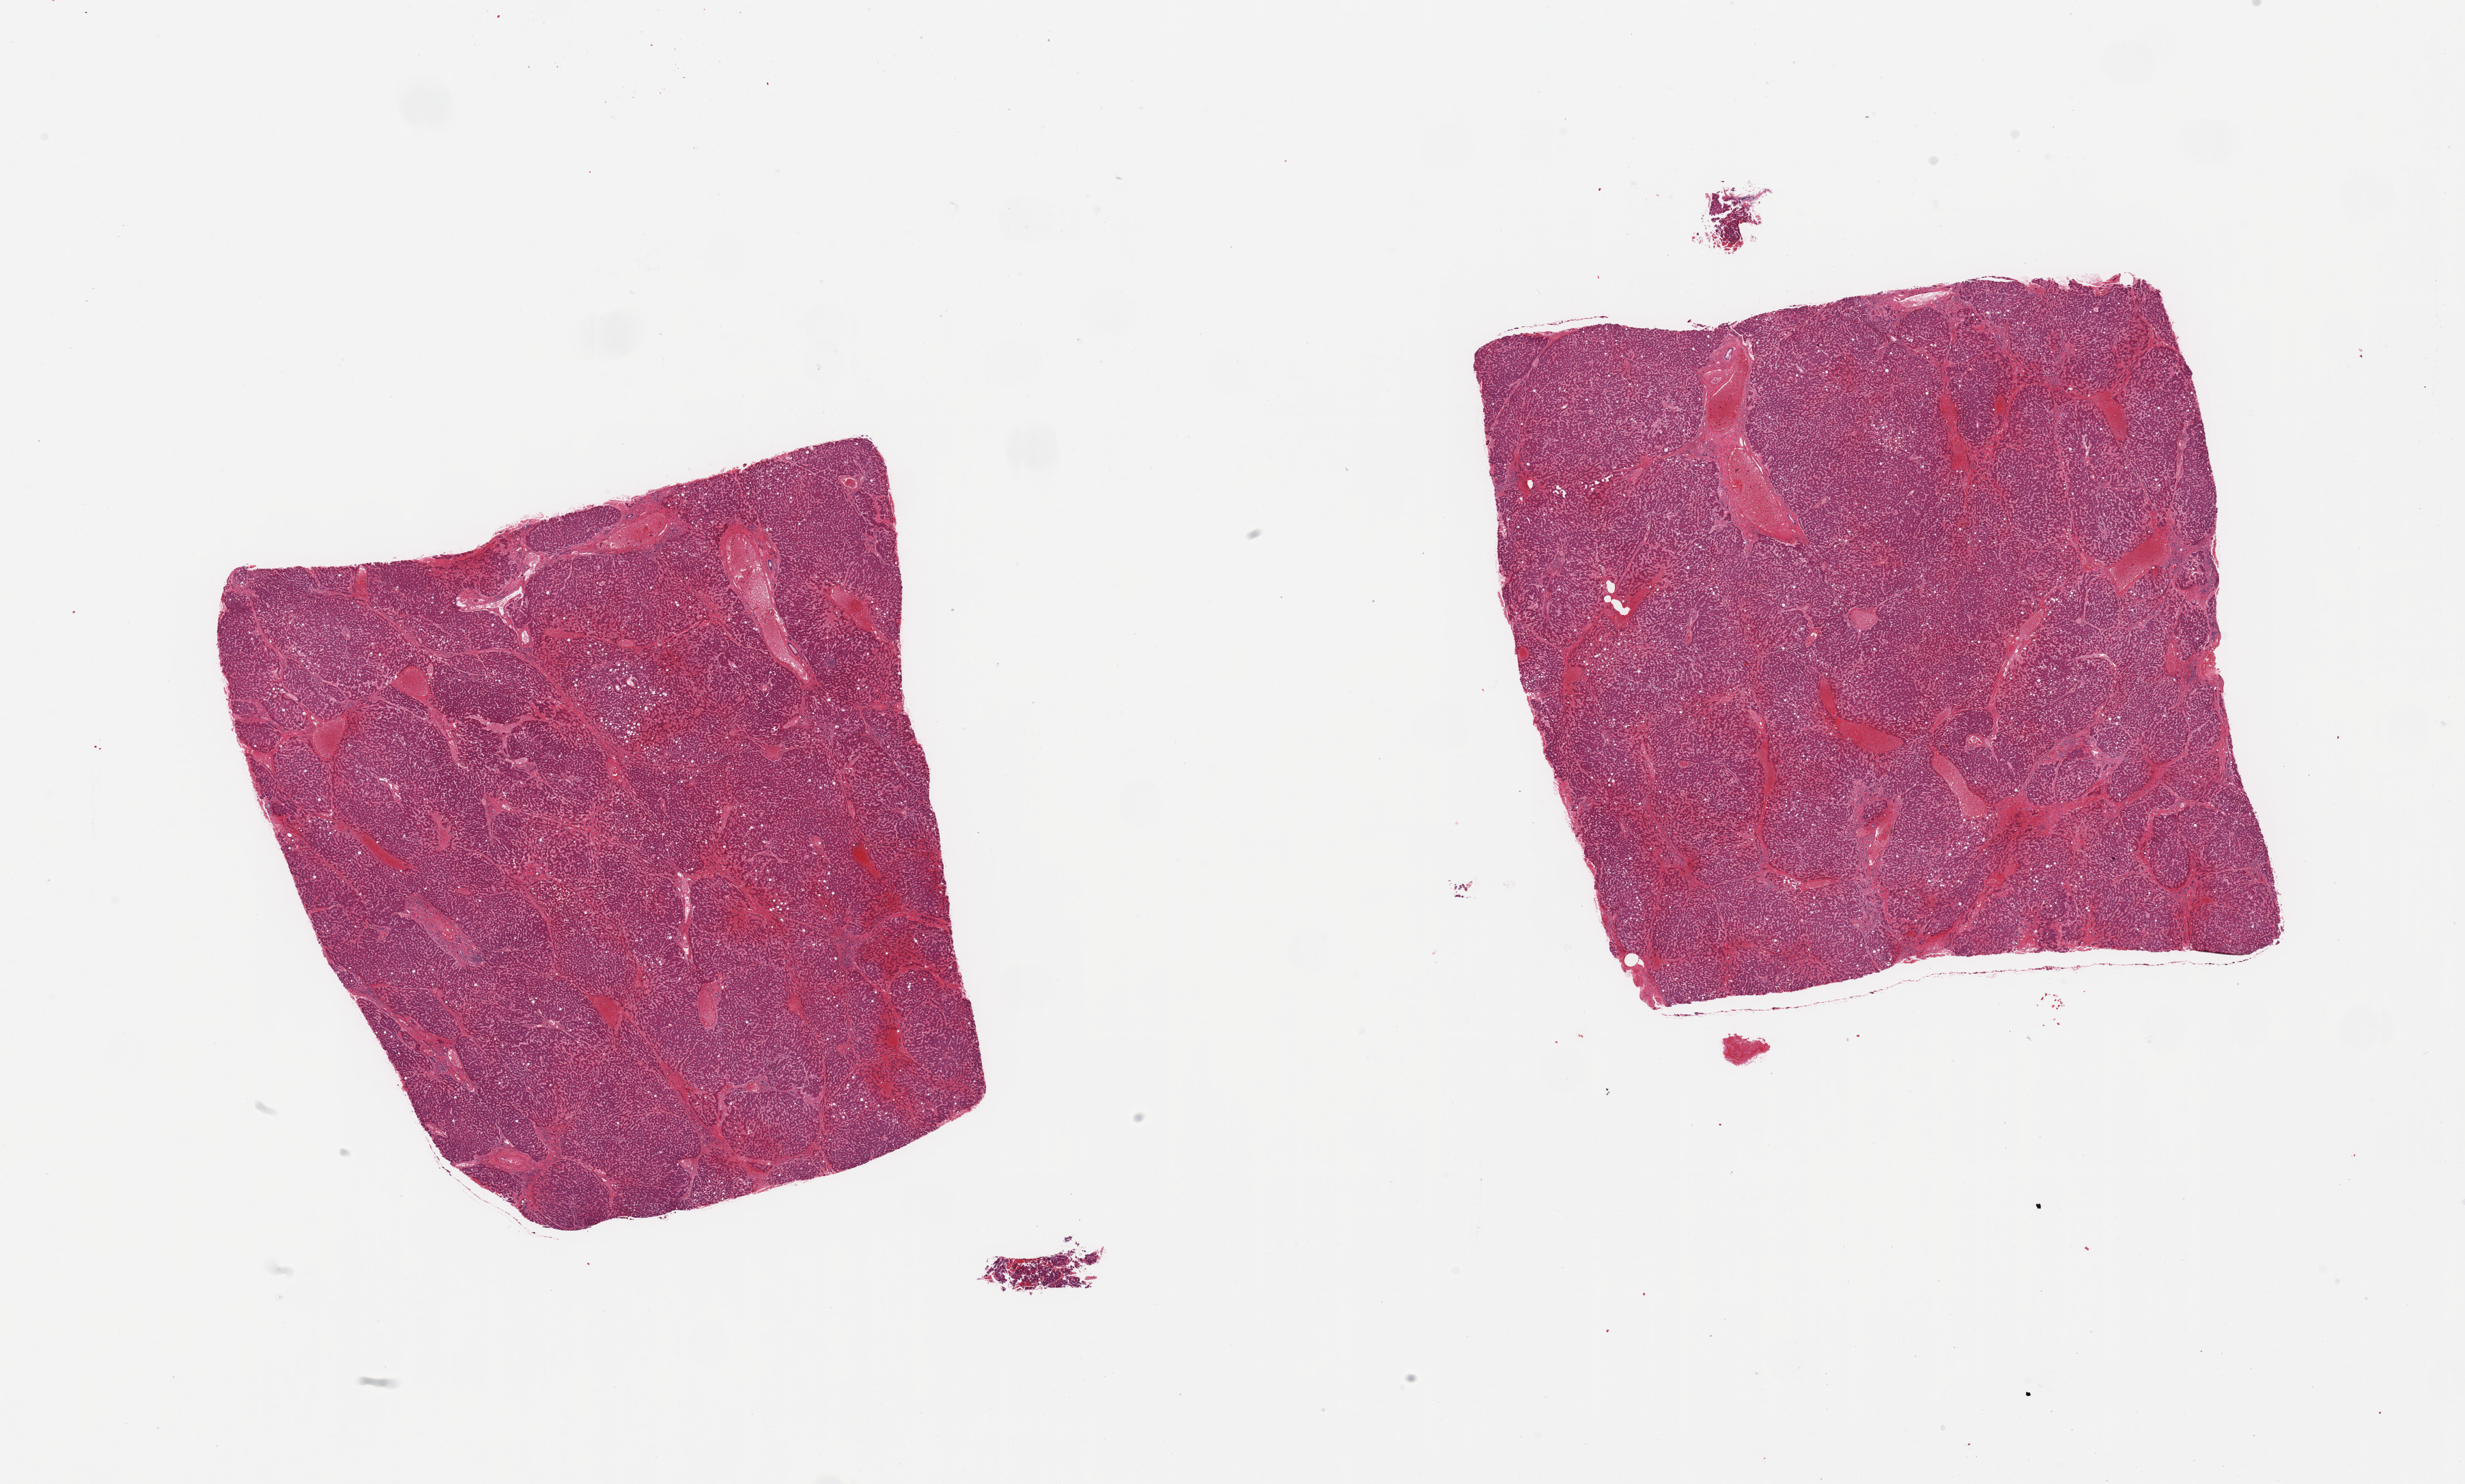
Hematoxylin and eosin (H&E) whole-slide image, shown as a low-resolution overview of the whole scanned area (about 28.5 x 17.2 mm); PAXgene-fixed, paraffin-embedded tissue; target tissue: liver; donor tissue sample. Donor: male.
Pathologist's review note for this sample: 2 pieces; bridging fibrosis; moderate venous & centrolobular congestion; 10% macrovesicular steatosis.